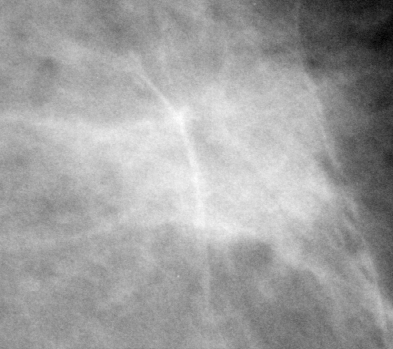
Region of interest cut from a scanned film mammogram (one marked finding), left breast, MLO view, BI-RADS breast density category 1 (scale 1–4).
Marked abnormality: mass, shape irregular, margins ill defined; BI-RADS assessment category 5; pathology (as recorded): malignant.